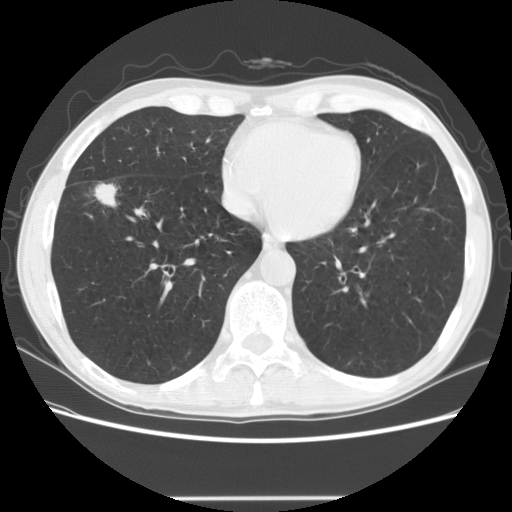
Low-dose screening chest CT, one axial slice; position 53 of 145 along the scan axis; reconstruction kernel STANDARD; 140 kVp; lung window (W 1500 / L -600 HU); 2.5 mm slice thickness; 512 × 512 image matrix, field of view 365 × 365 mm.
Annotated regions visible in this slice (expert manual segmentation):
- lesion 1 (tumor, middle lobe of right lung): bounding box [x1, y1, x2, y2] px = [94, 182, 118, 208]